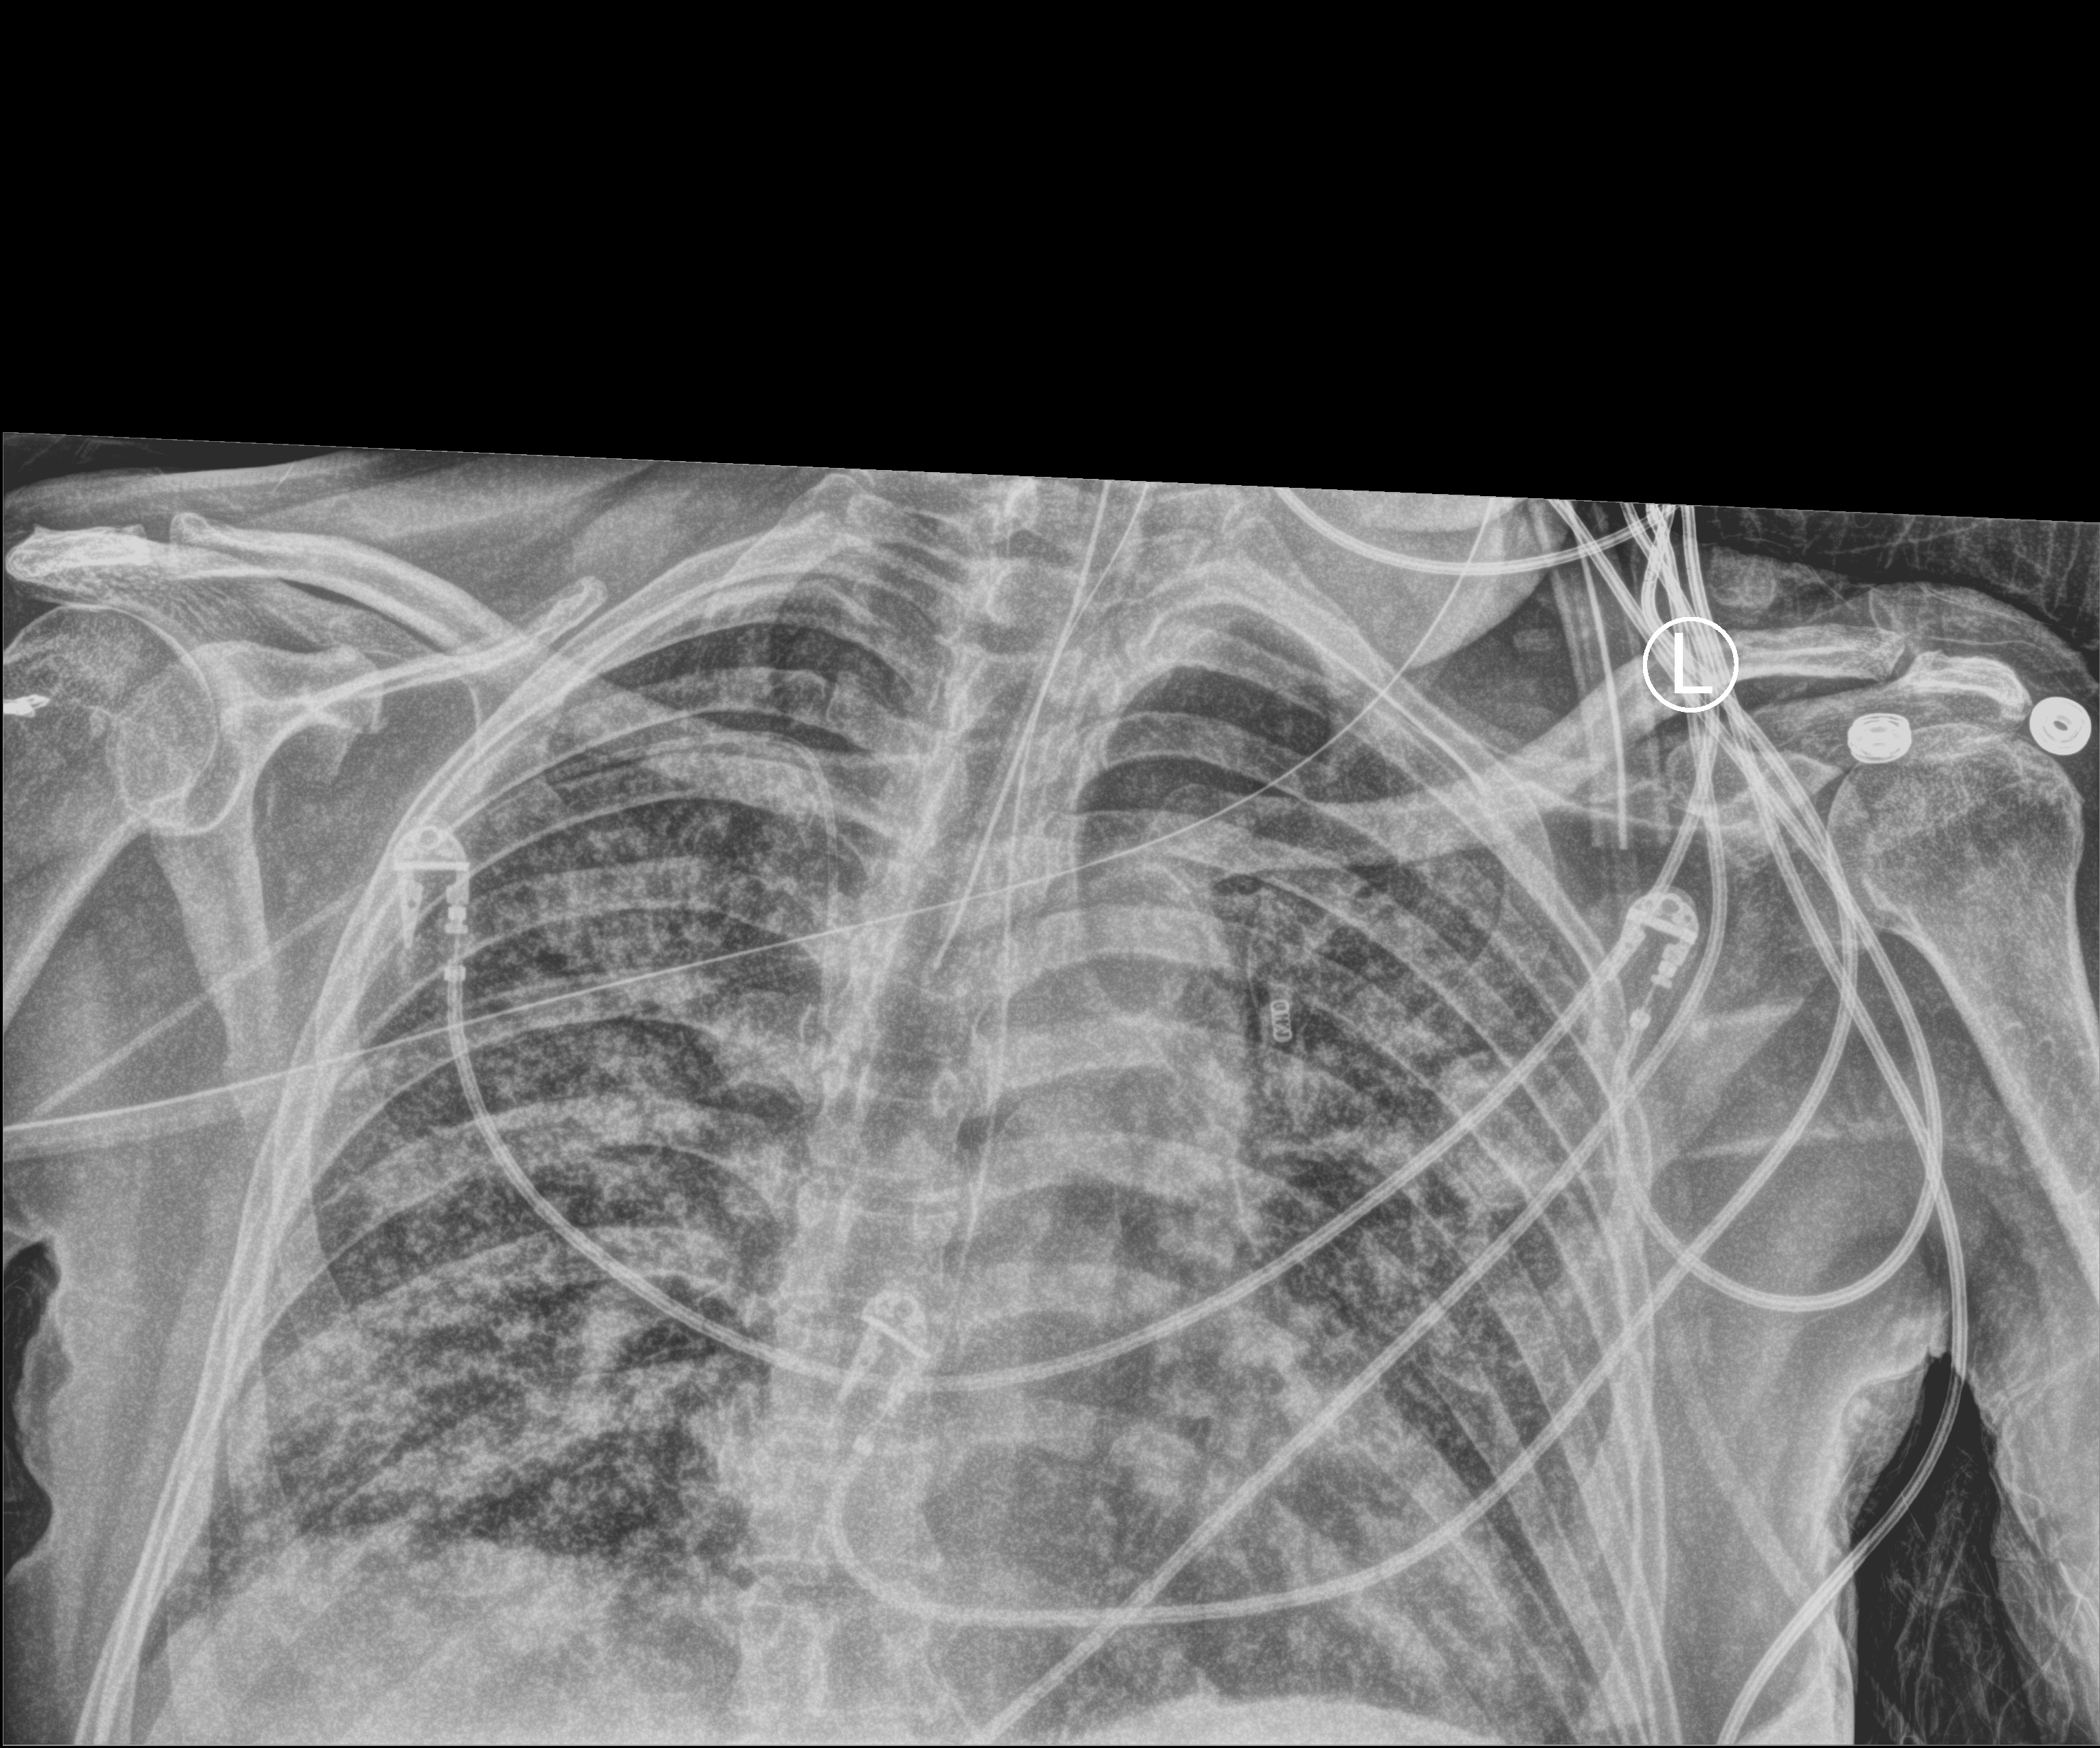
Portable chest radiograph. Male patient hospitalised with COVID-19, age 60–74 years.
Admission-level facts for this patient (not findings on this image; timing relative to this image not recorded):
- diabetes (admission record): no
- length of hospital stay: 65 days